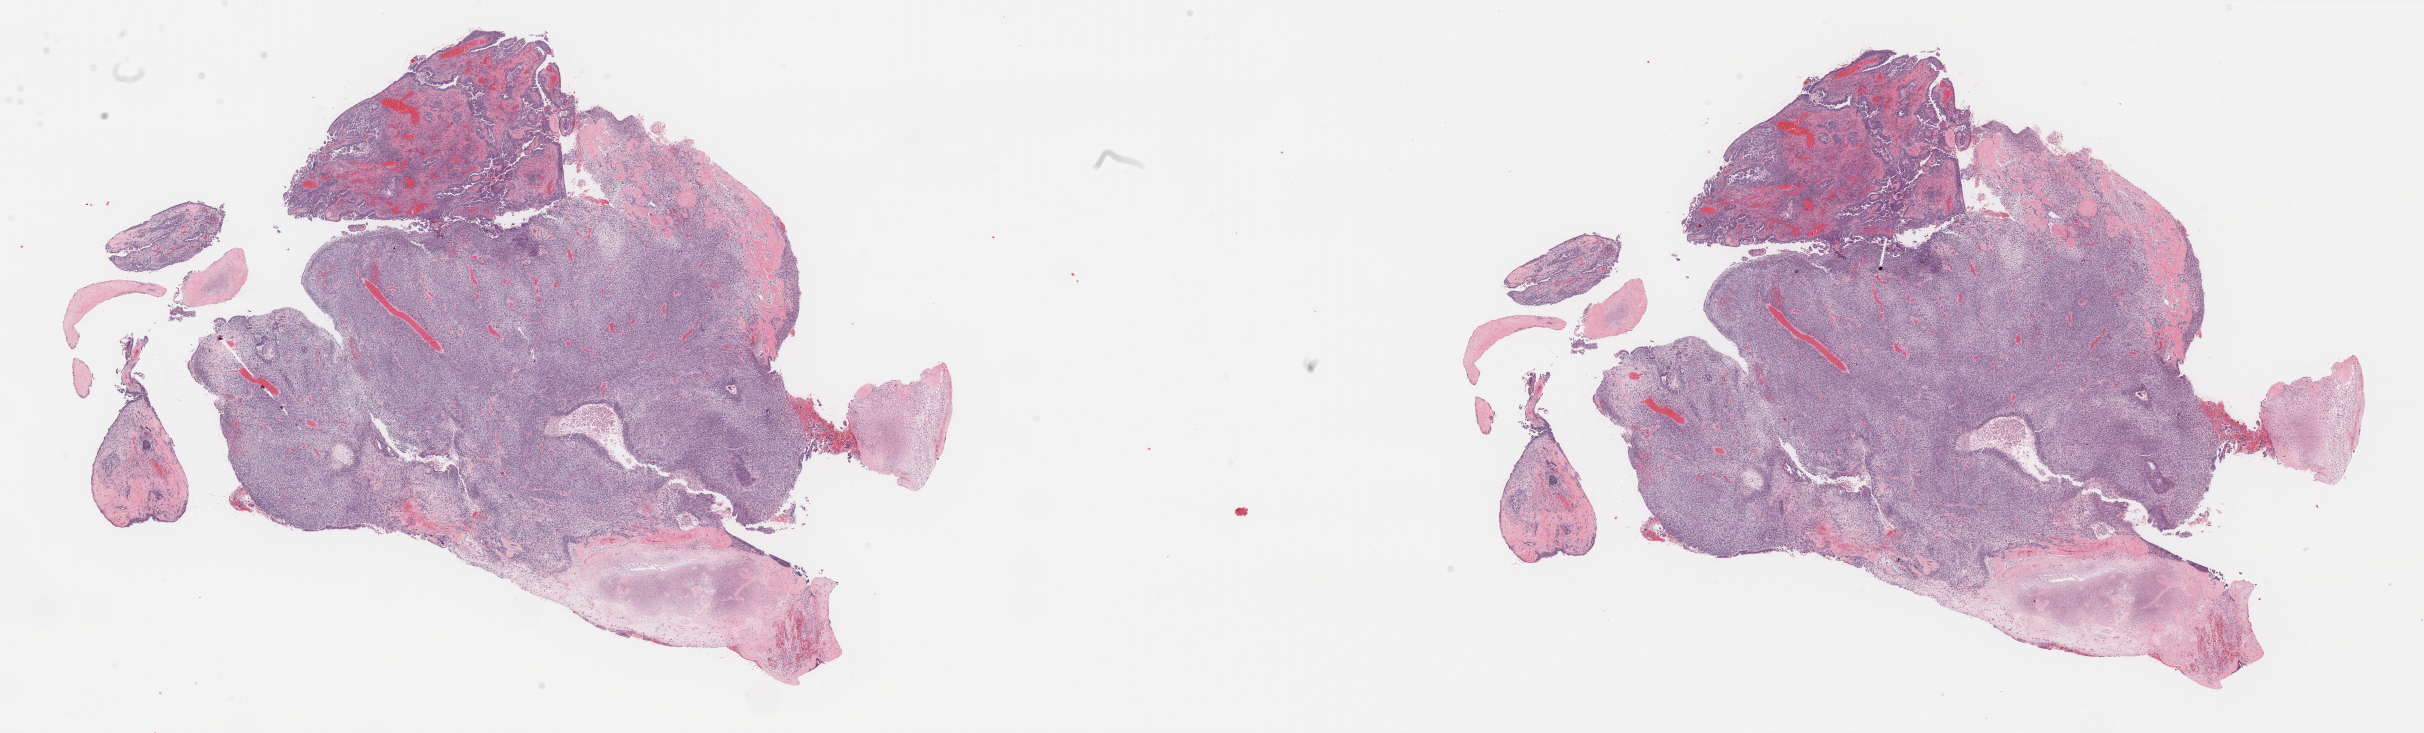
H&E whole-slide image, shown as a low-resolution overview of the whole scanned area (about 38.4 x 11.6 mm, slide scanned at 40x). Formalin-fixed paraffin-embedded (FFPE) diagnostic section. Primary tumour sample from the uterus. Patient: female, age at initial diagnosis 76 years.
FIGO stage: IIIC2. Pathologic diagnosis: Mullerian mixed tumor (endometrium).